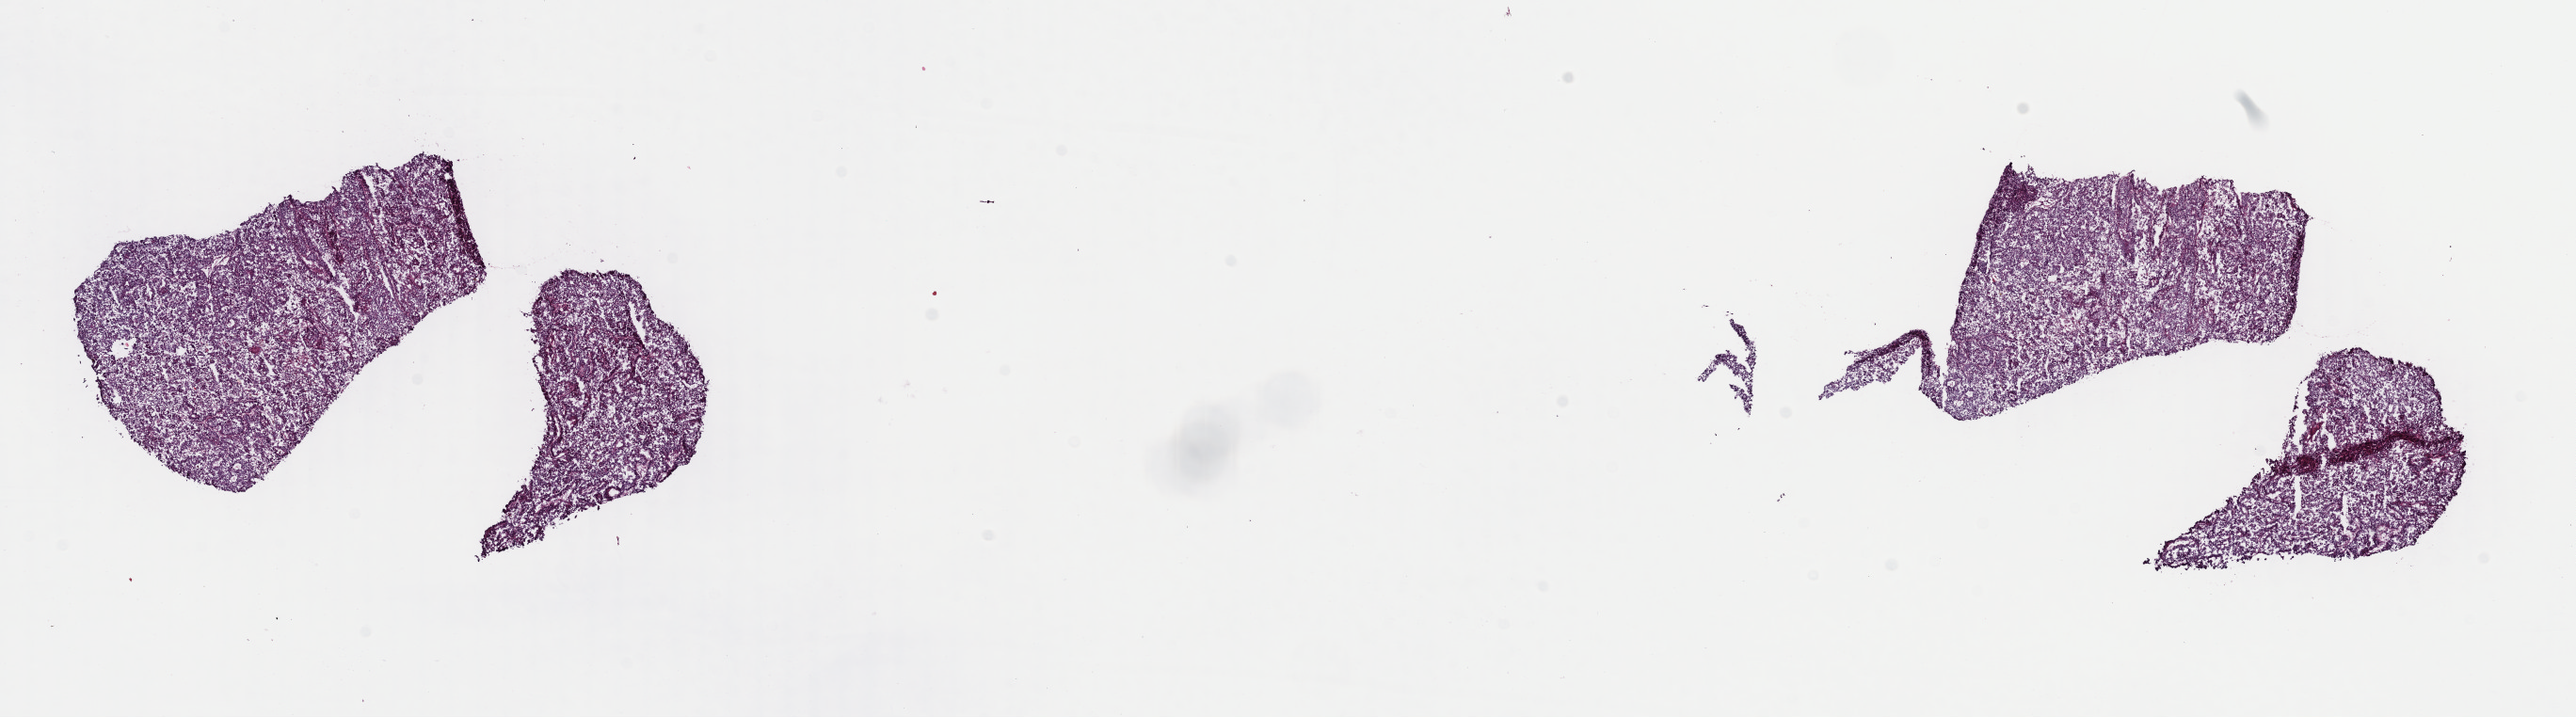
Whole-slide histology image, H&E-stained — low-resolution overview of the scanned area, about 21.6 x 6.0 mm, frozen section from the top of the tissue portion, primary tumour sample from the kidney. Male patient; age at initial diagnosis 59 years. Slide review estimates, as recorded: tumour cells 100%, tumour nuclei 93%, normal cells 0%, stromal cells 0%, necrosis 0%. Inflammatory infiltration, as recorded: lymphocyte infiltration 0%, monocyte infiltration 0%, neutrophil infiltration 0%.
Laterality: left. AJCC pathologic stage: IV (7th edition). Diagnosis: Papillary adenocarcinoma, NOS. Lymph nodes positive (case pathology): 0 of 1 examined.